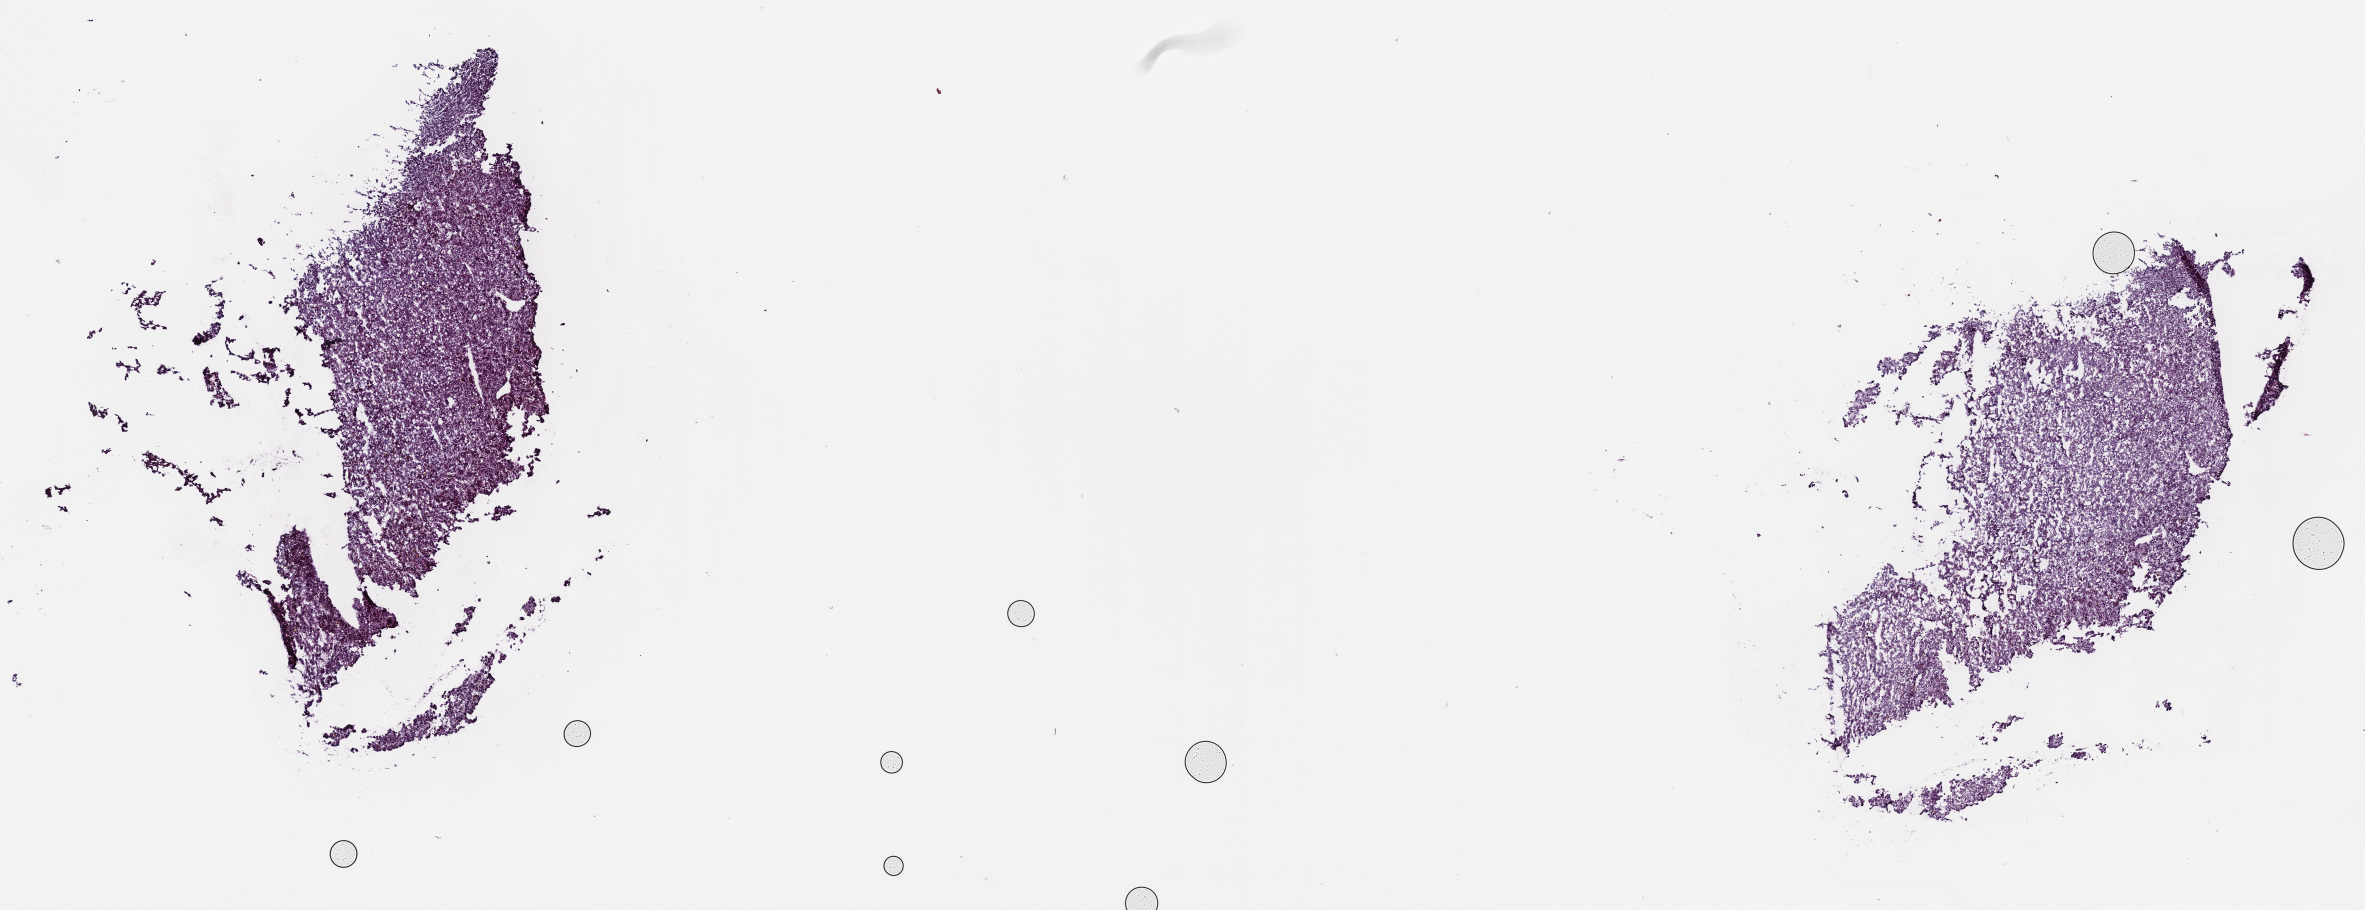
Whole-slide histology image, Hematoxylin and eosin (H&E) stained, shown as a low-resolution overview of the whole scanned area (about 19.1 x 7.4 mm, from a 40x scan); frozen section from the top of the tissue portion; primary tumour sample from the liver. Male patient; age at initial diagnosis 55 years. Histologic grade: G2 (moderately differentiated). Slide review estimates, as recorded: tumour cells 93%, tumour nuclei 95%, normal cells 0%, stromal cells 5%, necrosis 2%. Inflammatory infiltration, as recorded: lymphocyte infiltration 4%, monocyte infiltration 0%, neutrophil infiltration 0%.
Diagnosis: Hepatocellular carcinoma, NOS. AJCC pathologic stage: II.